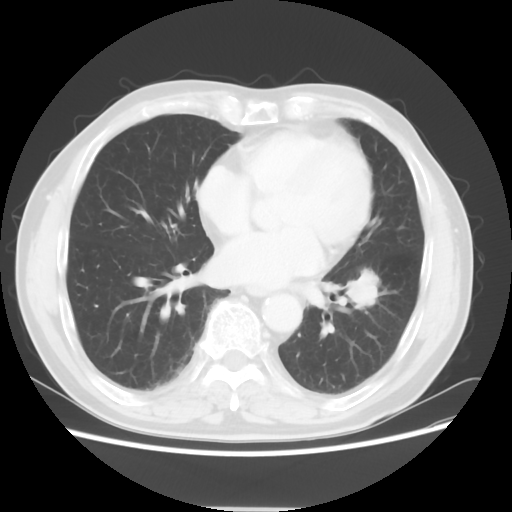
Chest CT, one axial slice. Position 24 of 64 along the scan axis. 120 kVp. Lung window (W 1500 / L -600 HU). 5 mm slice thickness. 512 × 512 image matrix, field of view 366 × 366 mm. Patient: male, 71 years. From the clinical record (not read from this slice): clinical TNM (as recorded): T1c N1 M0; histopathological grade: G2-3.
Annotated regions visible in this slice (bounding box drawn by a radiologist):
- lung tumour (recorded histology: adenocarcinoma): box from (x=339, y=253) to (x=388, y=315) px